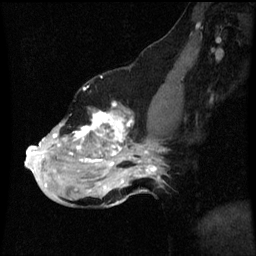
Breast MRI (dynamic contrast-enhanced), one sagittal slice. Position 35 of 60 along the scan axis. Dynamic contrast-enhanced series, image 2 of 3 at this slice position (ordered by acquisition). 1.5 T. TE 4.2 ms, TR 8.9 ms. 256 × 256 image matrix, field of view 200 × 200 mm. Patient: female, 49 years. Case-level facts recorded for this patient, not image findings: setting: breast cancer imaged before/during neoadjuvant chemotherapy; receptor status: HR-positive, HER2-negative.
Structures marked on this image (semi-automatically segmented with operator editing):
- analysis volume of interest (the breast-tissue region the enhancement analysis was run in; not a lesion): bounding box (x1, y1, x2, y2) in pixels: (26, 104, 159, 199)
- tumour enhancement mask (voxels above the 70 % enhancement threshold inside the analysis volume of interest): (26, 104, 157, 187)